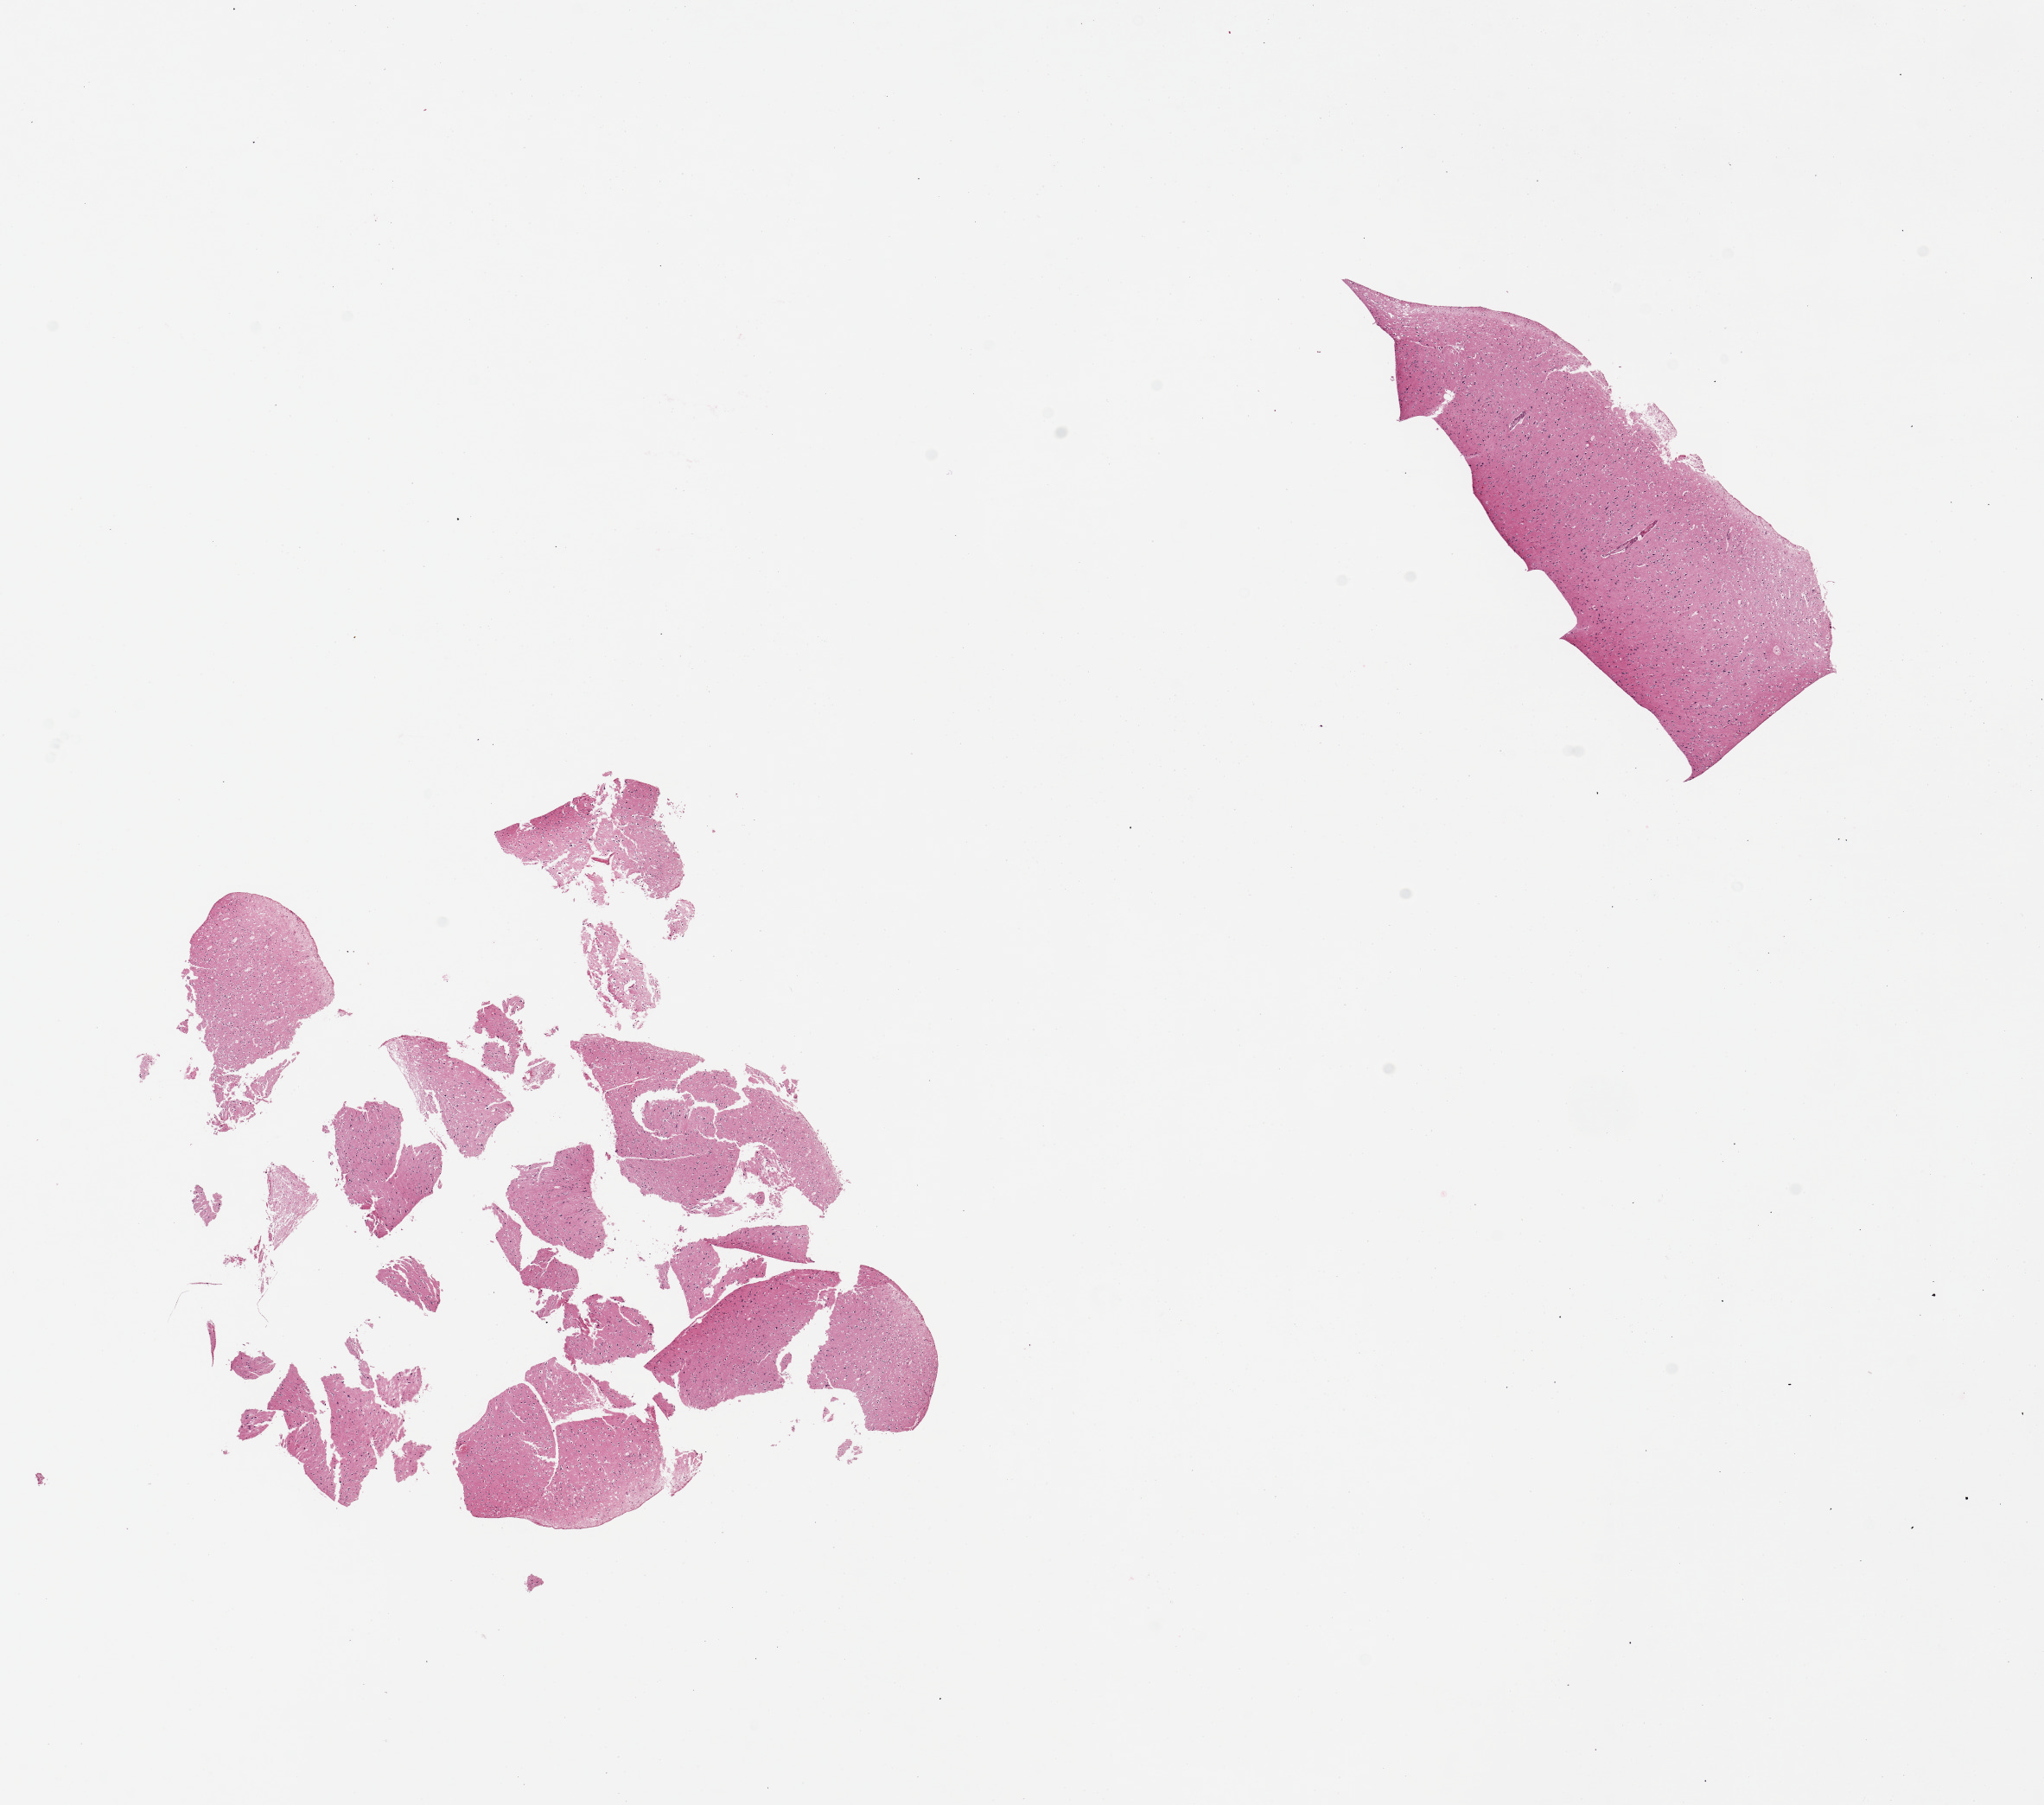
Whole-slide image, haematoxylin and eosin stain, brightfield, a low-resolution overview of the entire scanned area, about 18.7 x 16.5 mm, PAXgene-fixed paraffin-embedded (PFPE) section, section of cerebral cortex (target tissue), tissue donor sample. Donor: male.
- review note (as recorded): 2 pieces 5 x 2 mm and the second is composed of multiple fragments estimated to 5 x 5 mm in aggregate dimension